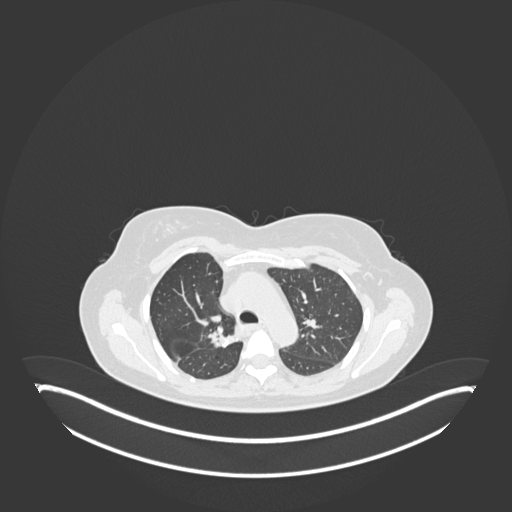
Chest CT, one axial slice; 120 kVp; lung window (W 1500 / L -600 HU); 1 mm slice thickness; 512 × 512 image matrix, field of view 500 × 500 mm. Female patient, age 65 years. Case-level facts recorded for this patient, not image findings: clinical TNM (as recorded): T1b N0 M0.
Outlined on this slice (bounding box drawn by a radiologist):
- lung tumour (recorded histology: adenocarcinoma): bounding box <204,325,241,353> (left, top, right, bottom; pixels)